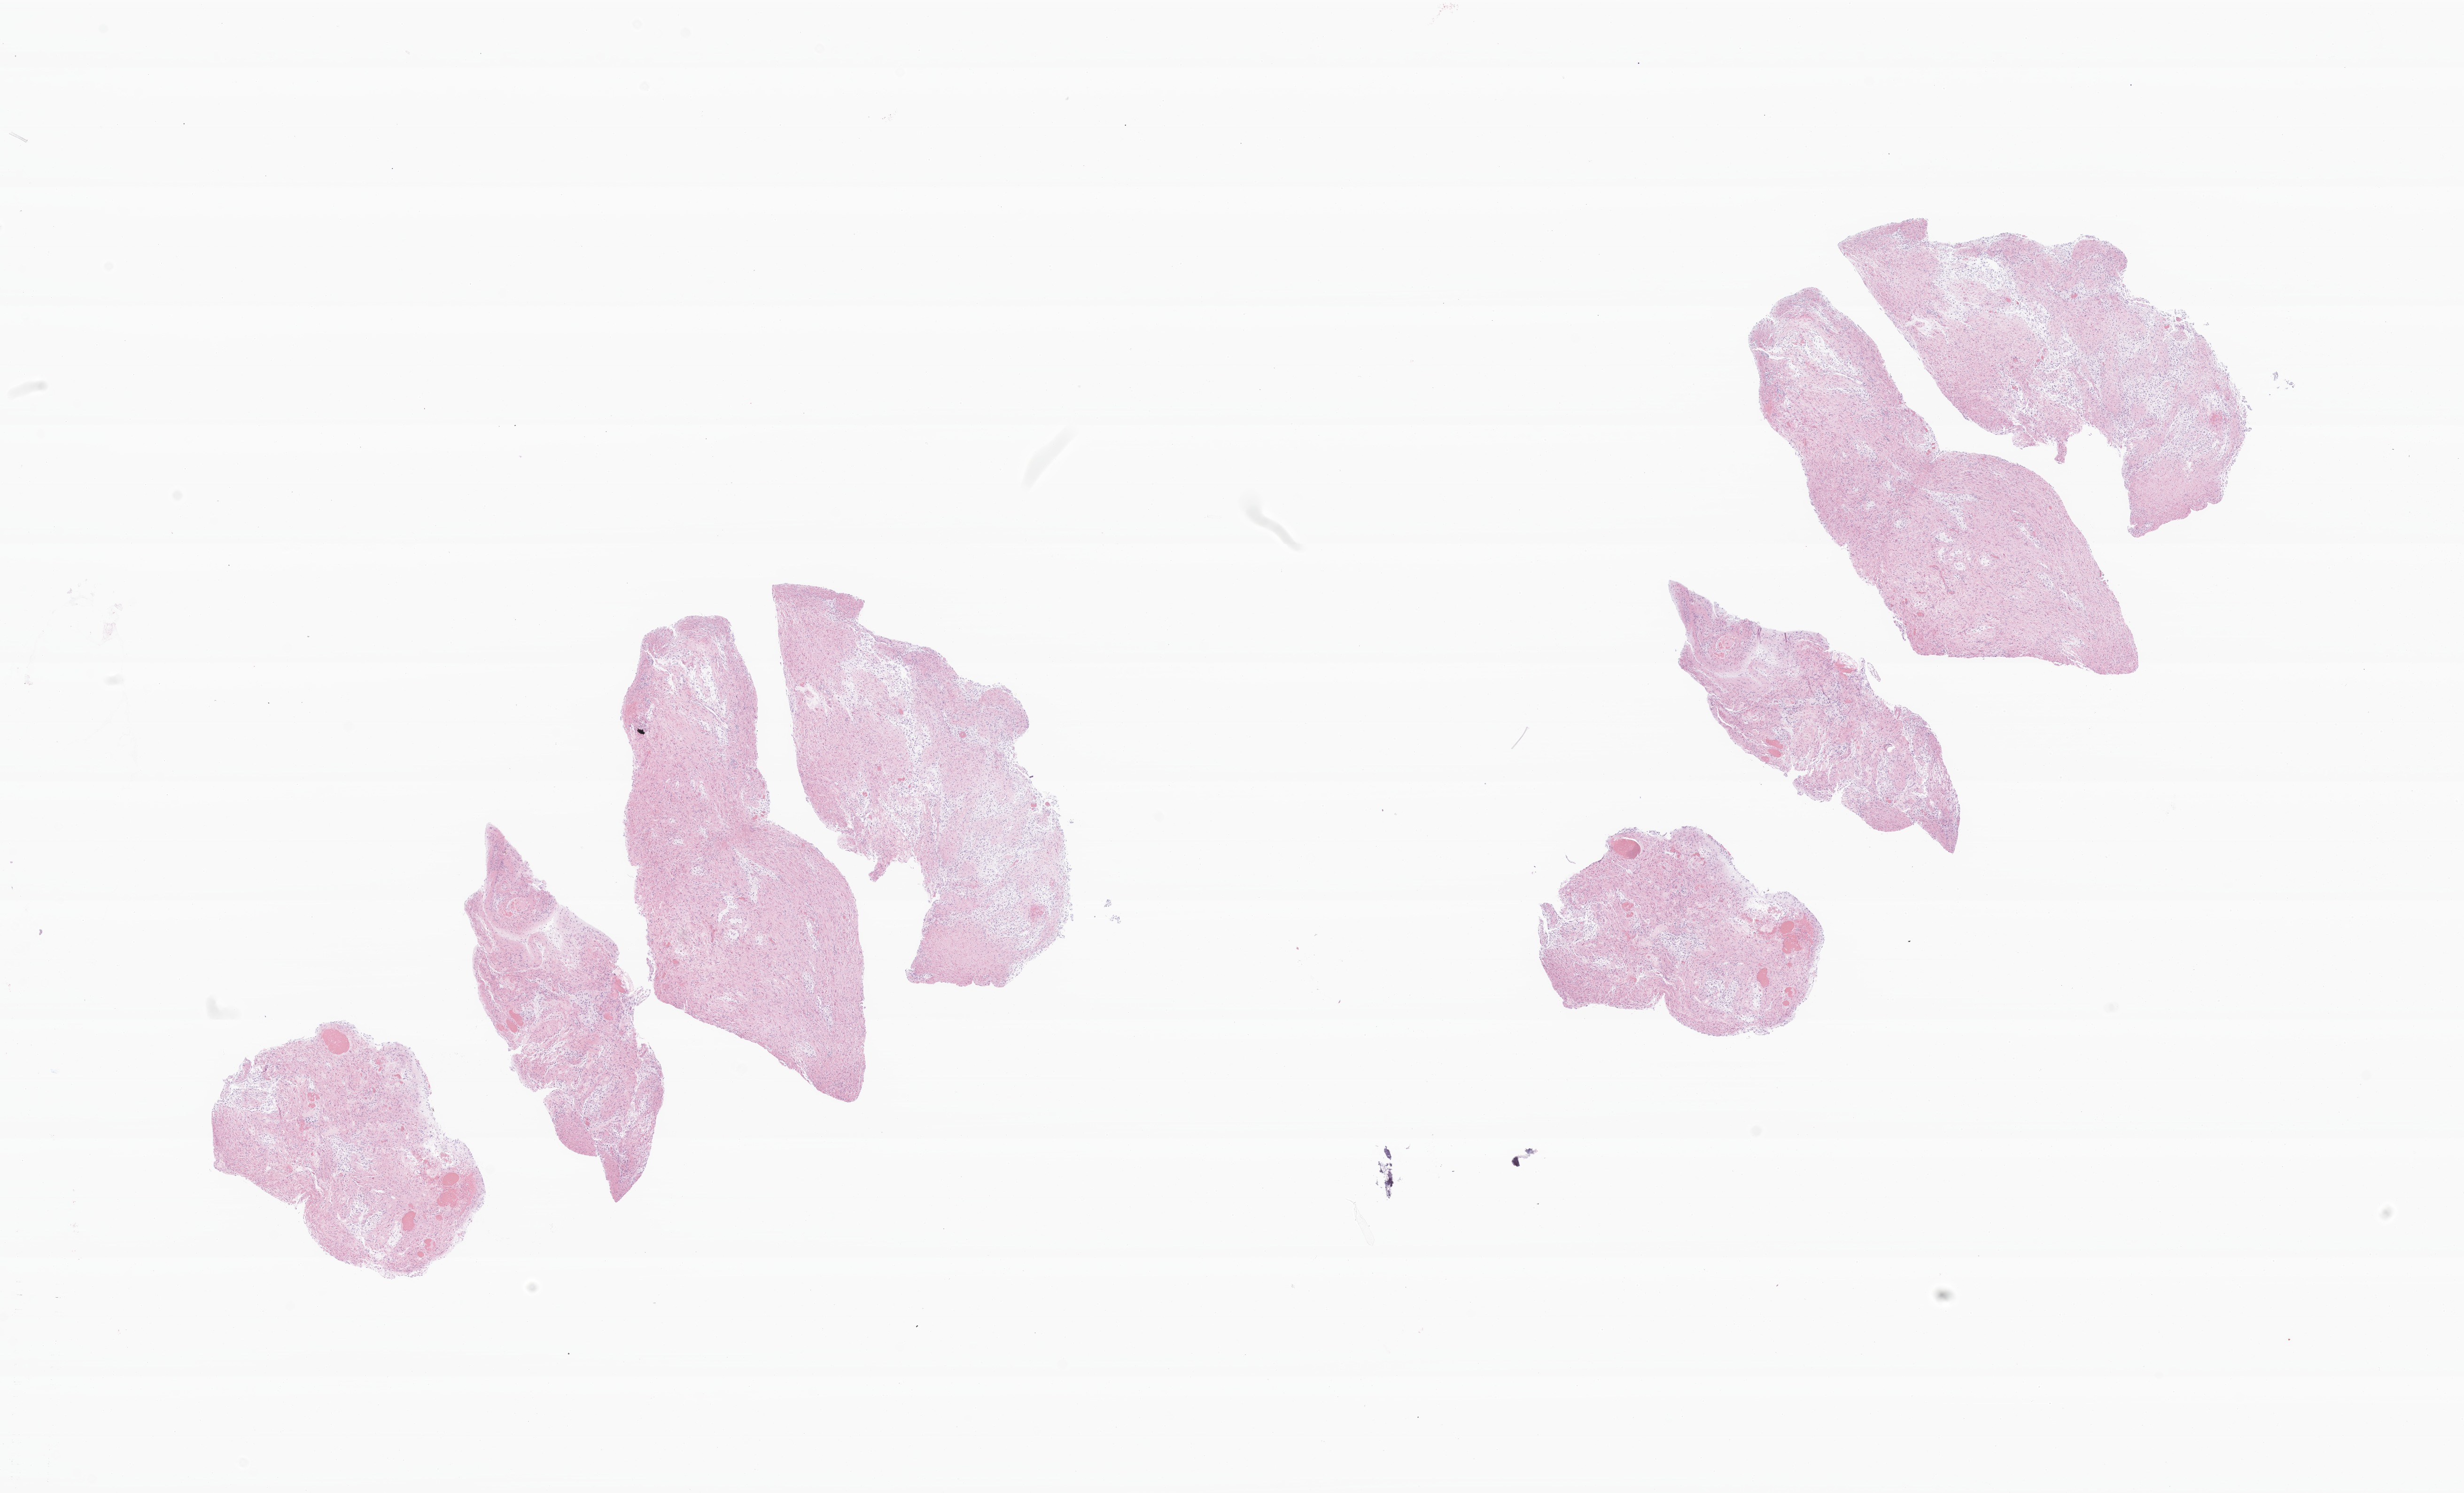
H&E whole-slide image of tumor tissue from the brain — whole scanned area (about 22.1 x 13.4 mm) shown as a low-resolution overview, formalin-fixed, paraffin-embedded (FFPE) tissue. Patient: male, age 186 months (15 years 6 months).
Recorded diagnosis: Pilocytic astrocytoma.